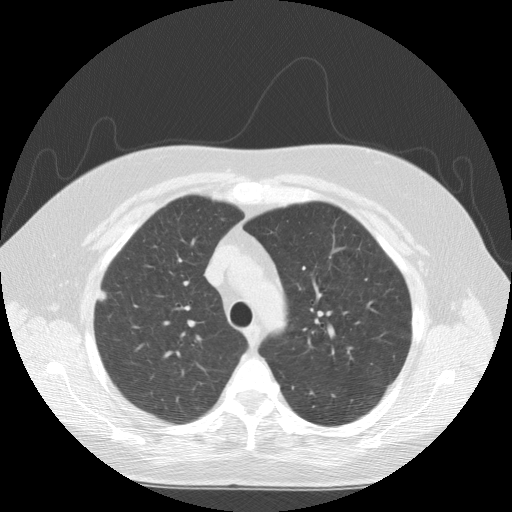
Low-dose screening chest CT, one axial slice. Slice 111 of 146 in the series (ordered by position). Reconstruction kernel STANDARD. Lung window (W 1500 / L -600 HU). 512 × 512 image matrix, field of view 370 × 370 mm.
Annotated regions visible in this slice (expert manual segmentation):
- lesion 1 (tumor, upper lobe of right lung): bounding box [x1, y1, x2, y2] px = [97, 290, 106, 301]